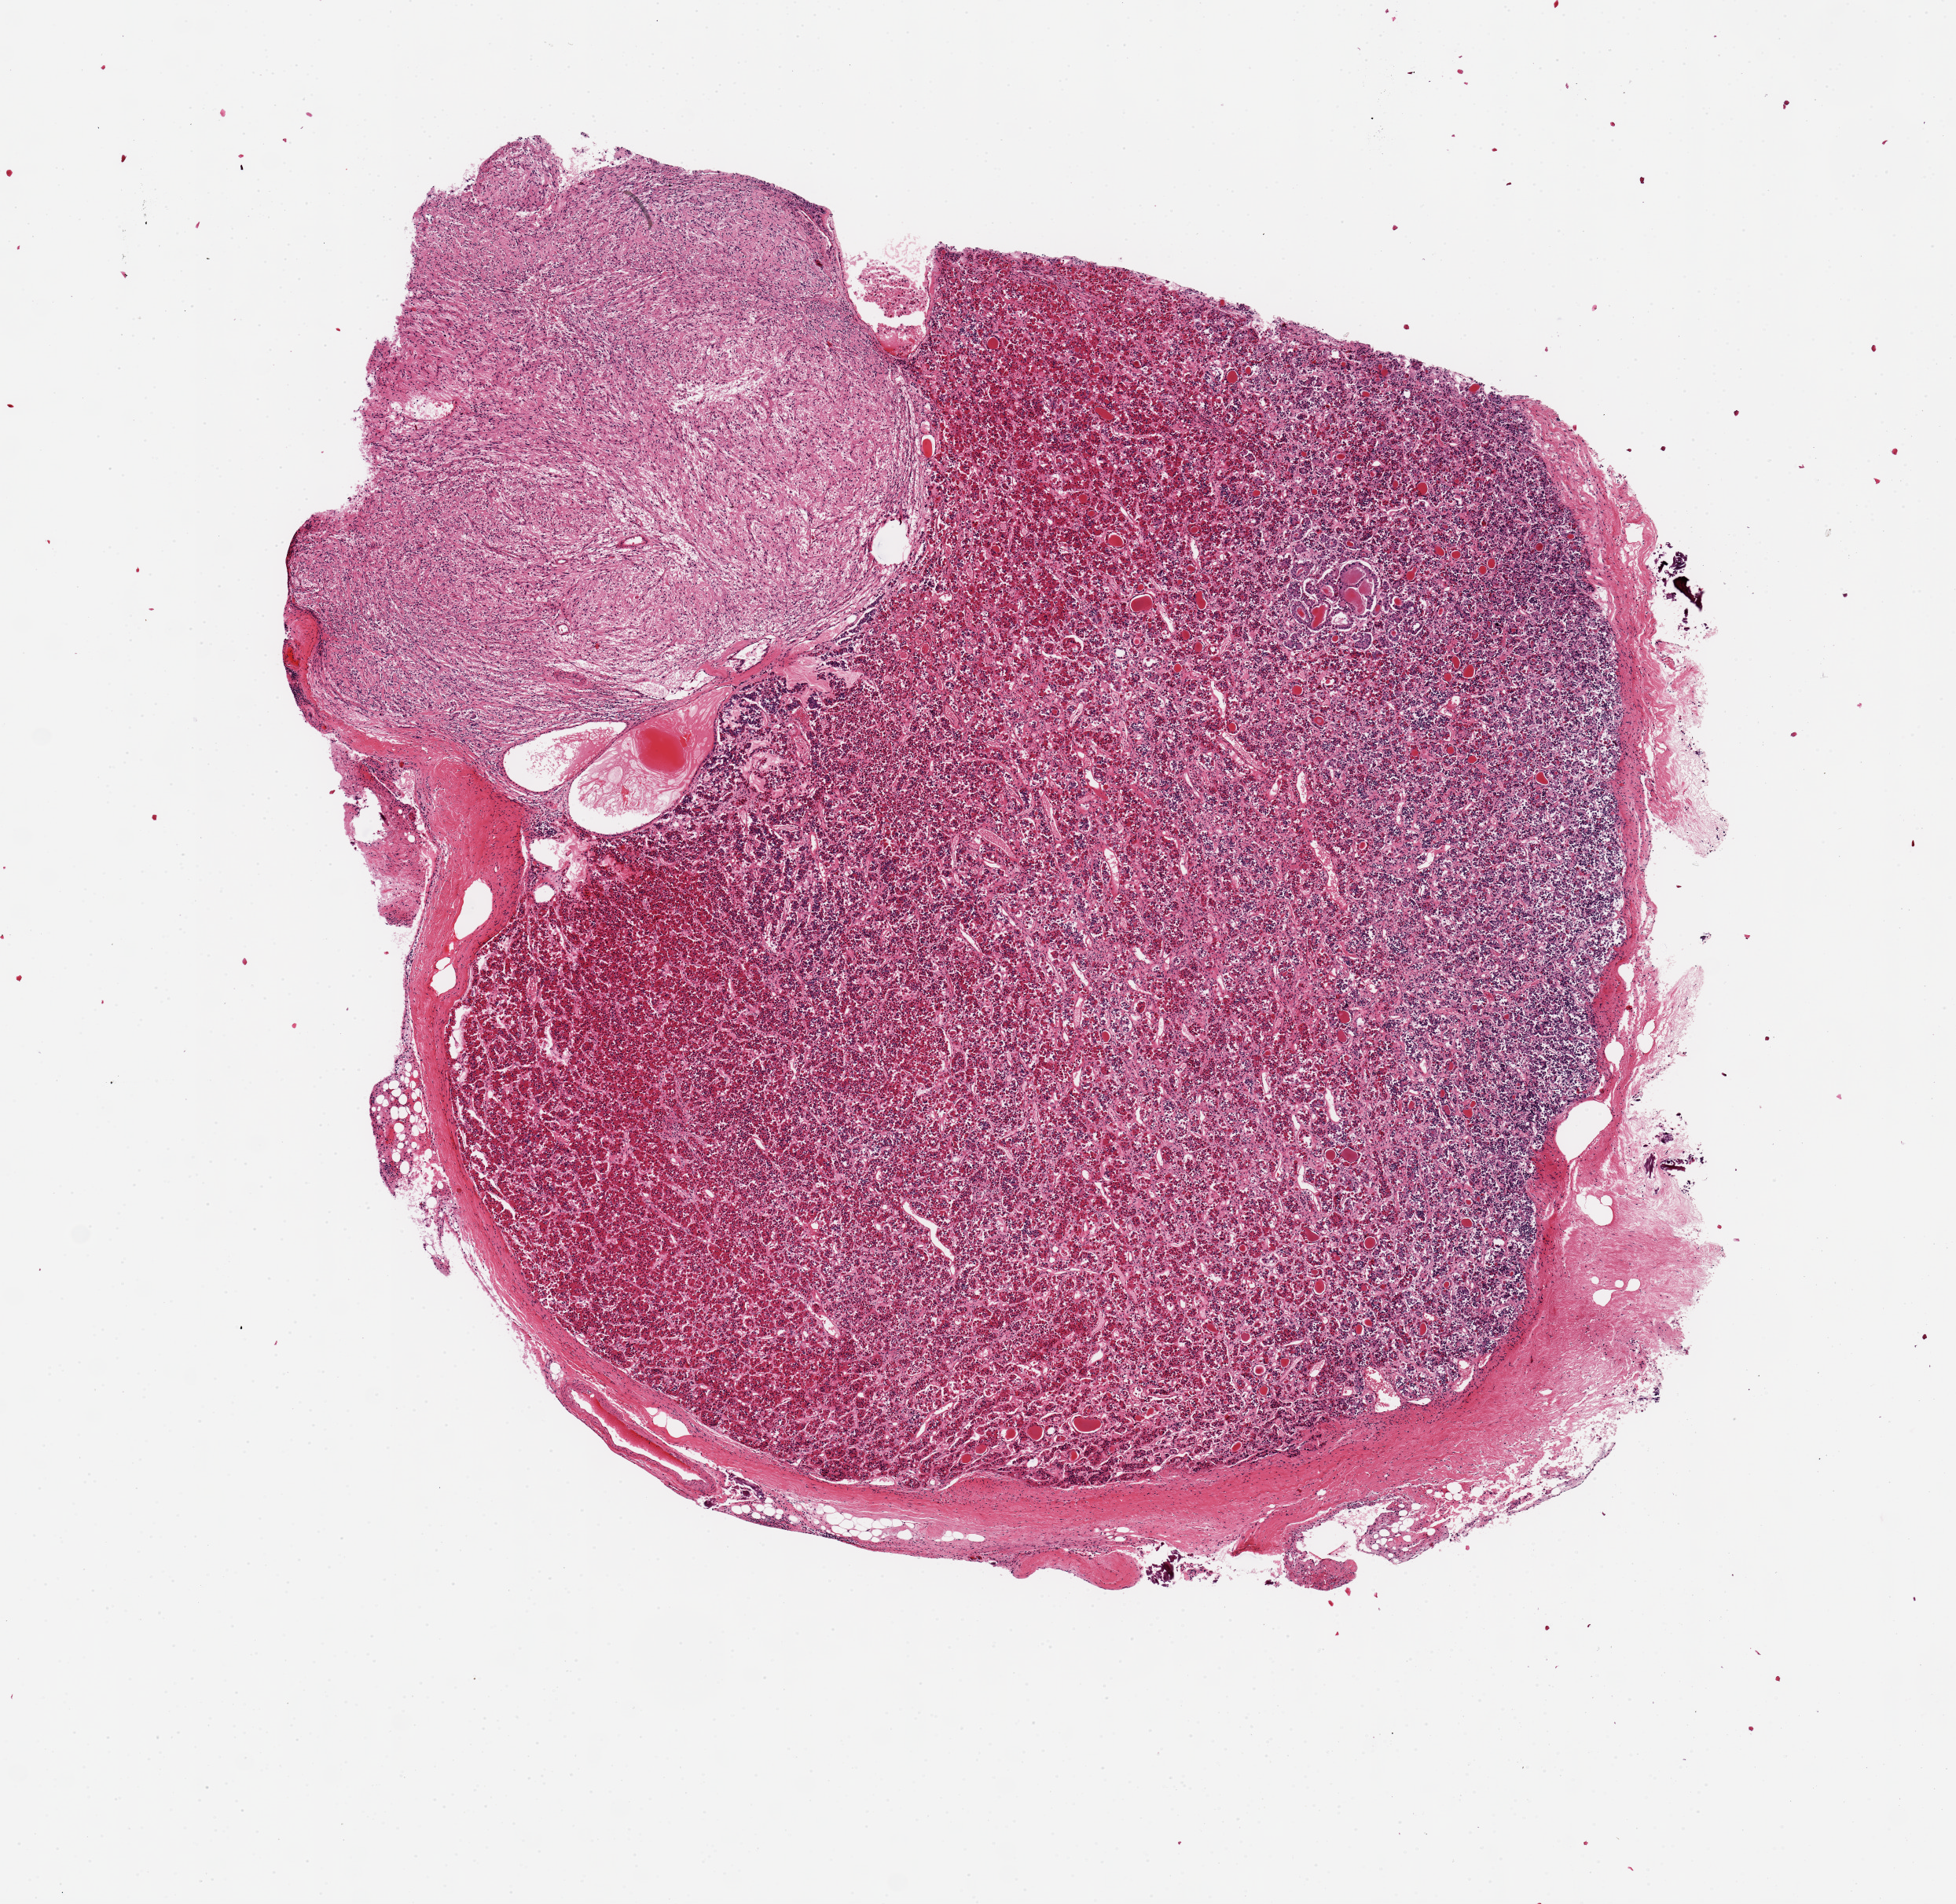
H&E whole-slide image, shown as a low-resolution overview of the whole scanned area (about 9.8 x 9.6 mm), PAXgene-fixed, paraffin-embedded tissue, sampled site (target tissue): pituitary, tissue donor sample. Donor sex: female.
Review note (as recorded): A ~ 7x6.6 mm aliquot, with a 6.5x4.2 mm adenohypophysis and a ~3.2x2.5mm neurohypophysis/stalk fragment.